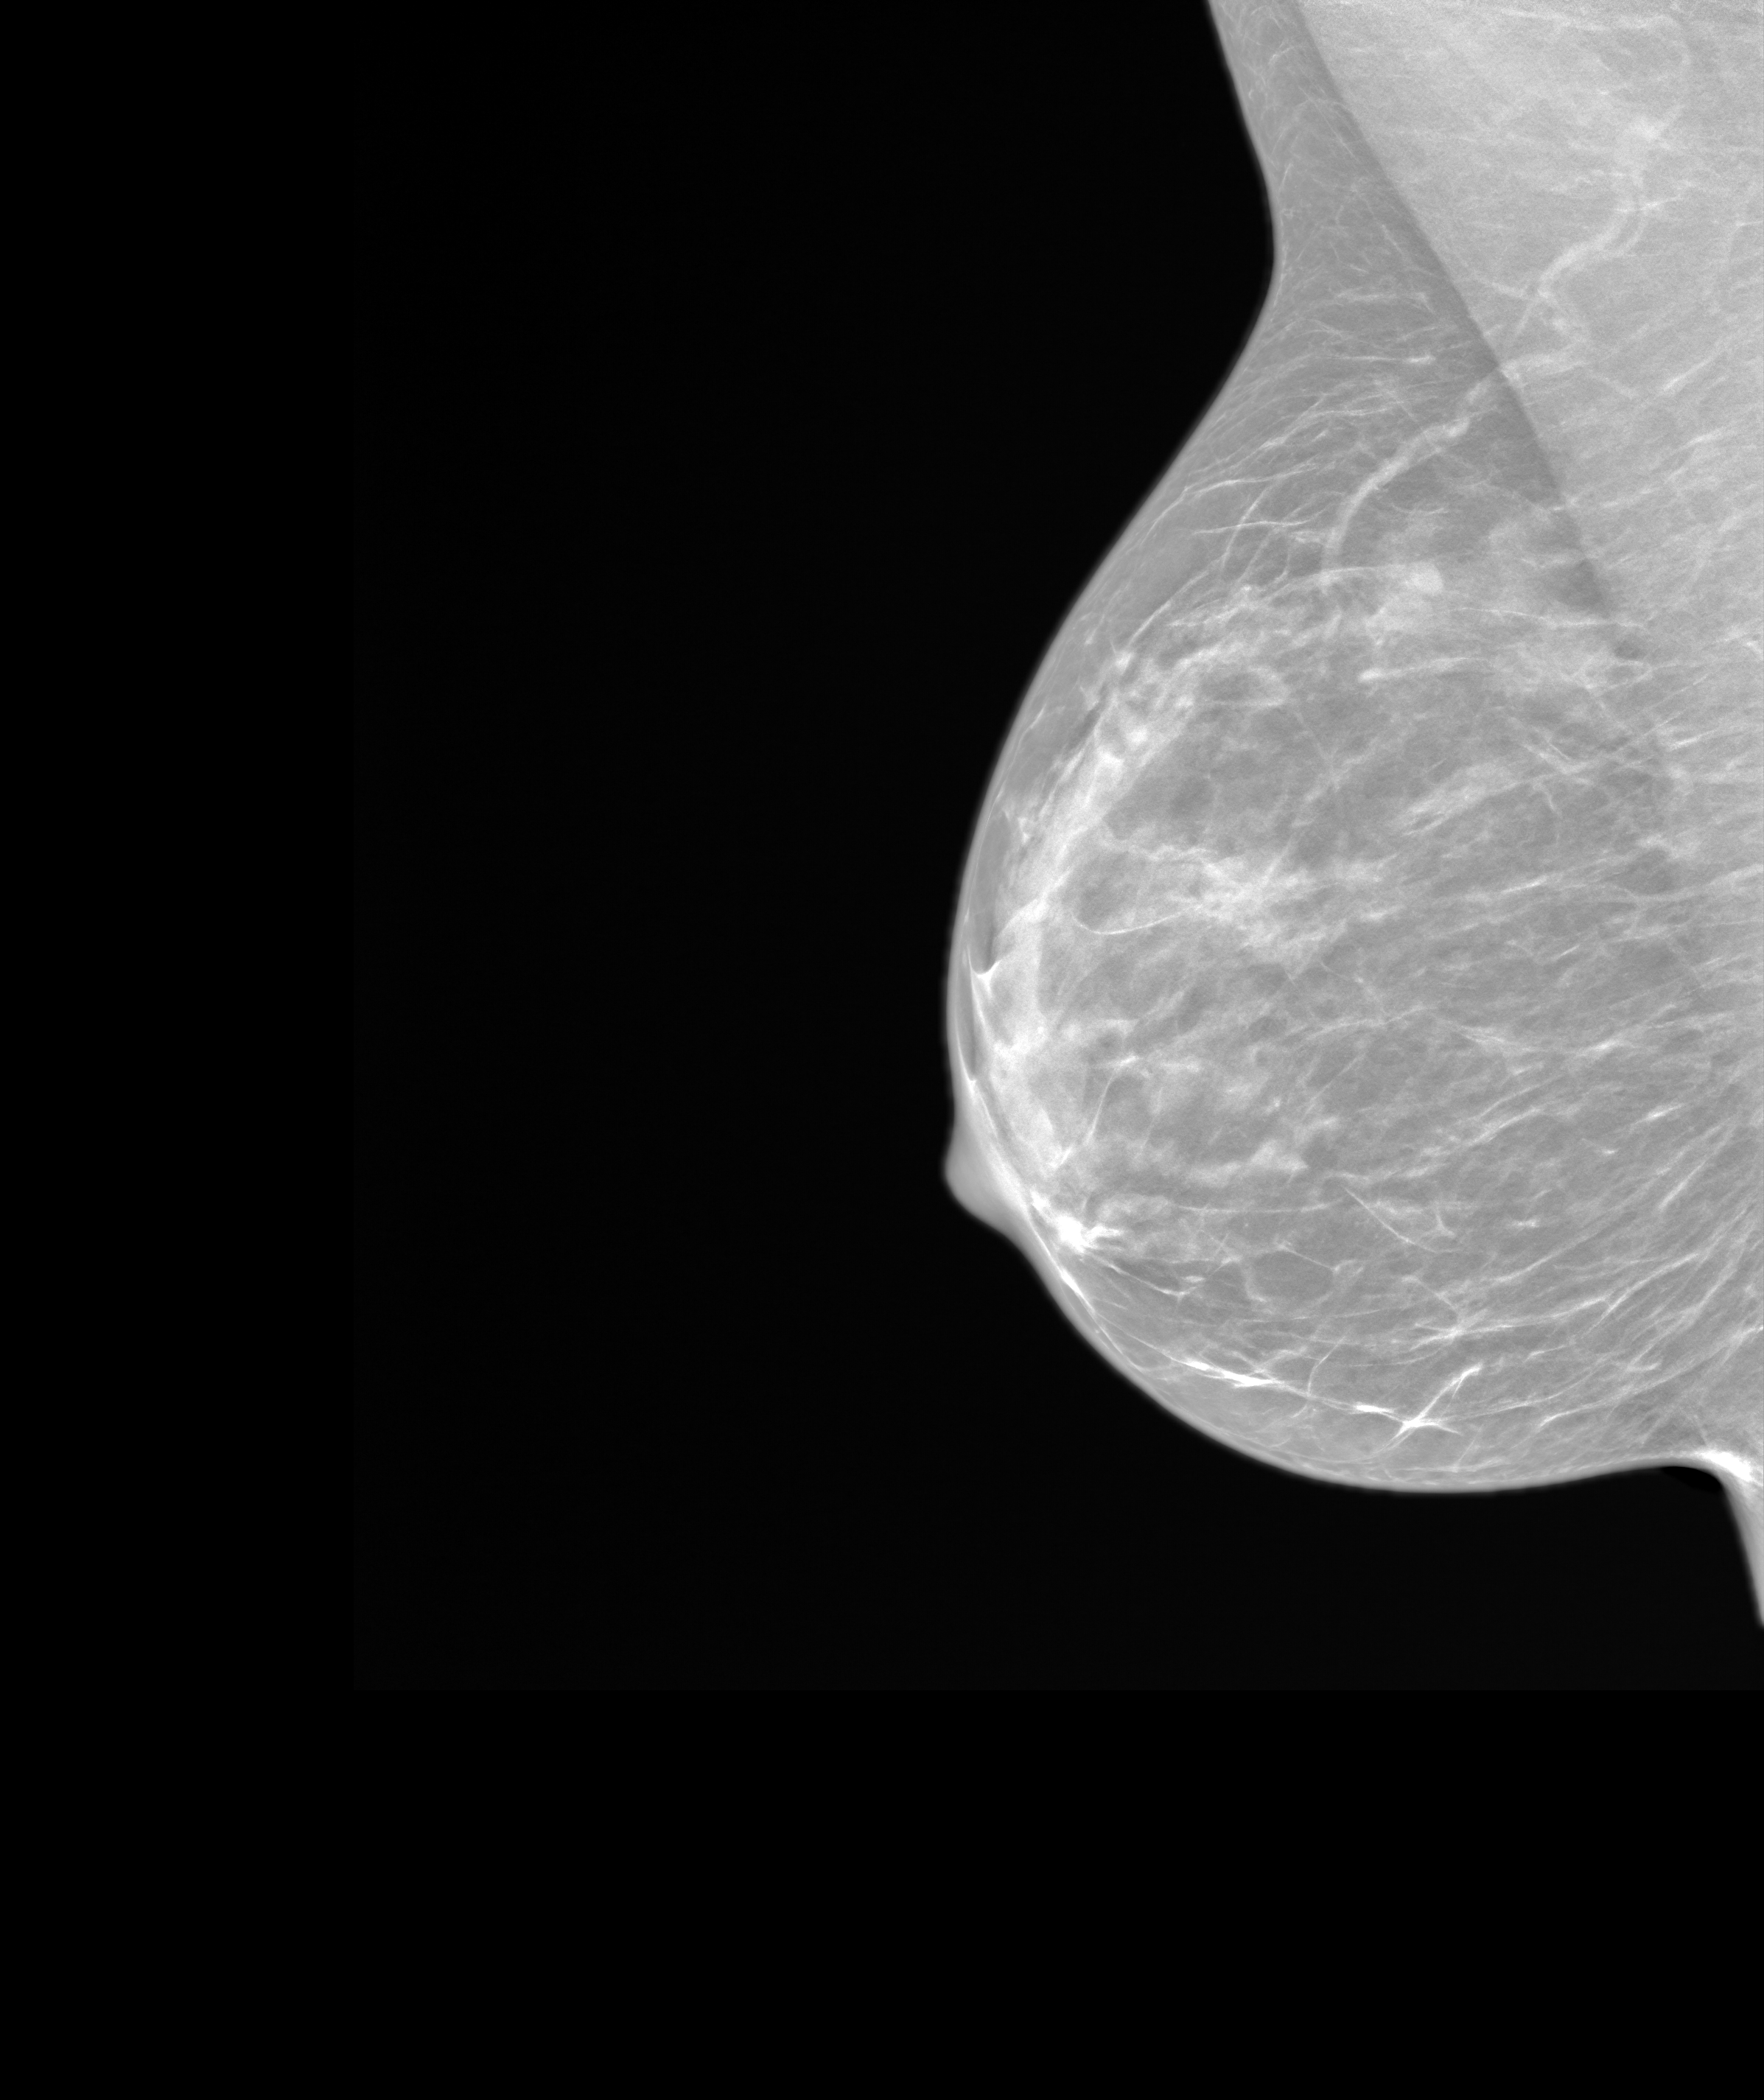
Synthesized 2-D mammogram reconstructed from digital breast tomosynthesis, right breast, MLO view, screening examination. Patient: female, 43 years.
Final BI-RADS assessment for this screening round (tomosynthesis exam, both breasts): category 1.